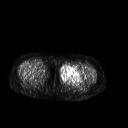
FDG PET of an extremity soft-tissue mass (from a PET/CT study), one axial slice; position 236 of 267 along the scan axis; 3.27 mm slice thickness; 128 × 128 image matrix, field of view 500 × 500 mm. Female patient, age 42 years. From the clinical record (not read from this slice): histological type: pleiomorphic leiomyosarcoma; grade: intermediate; site of the primary tumour: left thigh.
Outlined on this slice (expert contour drawn on MRI and transferred to this co-registered scan by the dataset authors):
- gross tumour volume including surrounding oedema: bounding box [x1, y1, x2, y2] px = [59, 64, 83, 83]
- gross tumour volume (mass): [59, 65, 82, 83]